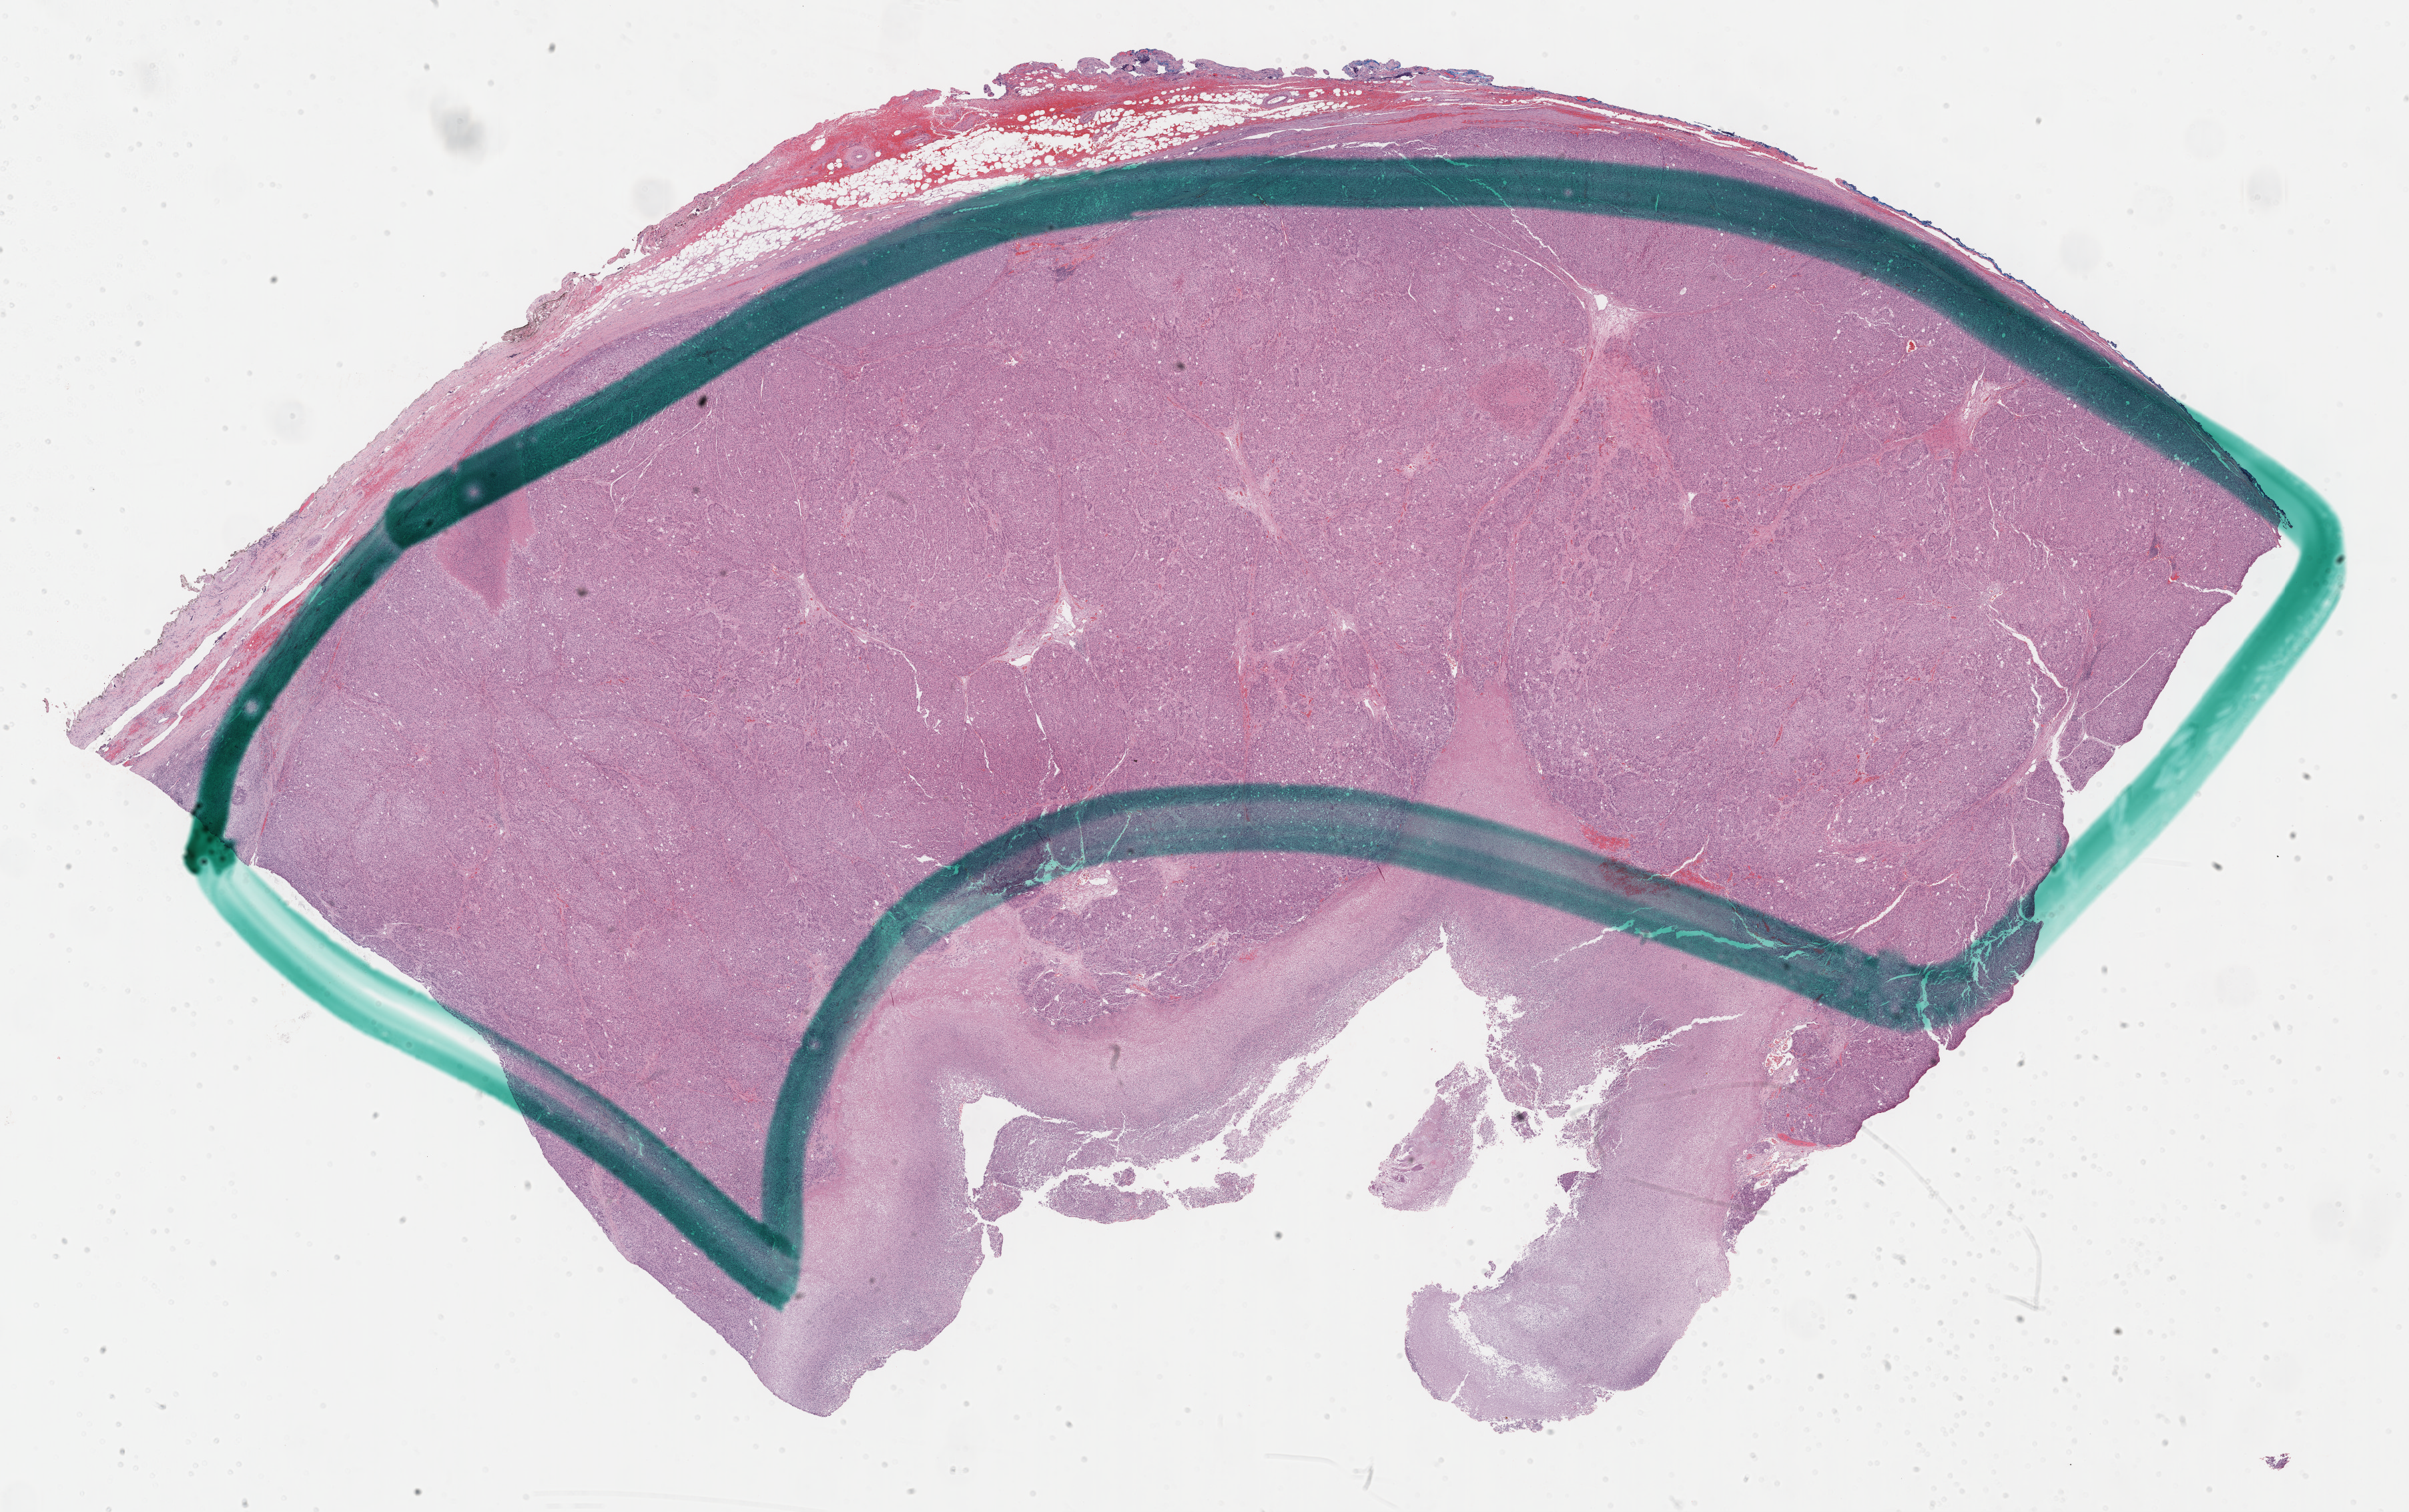
Digitized Hematoxylin and eosin (H&E) stained tissue section (whole slide), whole scanned area (about 29.2 x 18.3 mm) shown as a low-resolution overview; FFPE section; sample: primary tumour, adrenal cortex. Female patient; age at initial diagnosis 65 years.
Diagnosis: Adrenal cortical carcinoma.